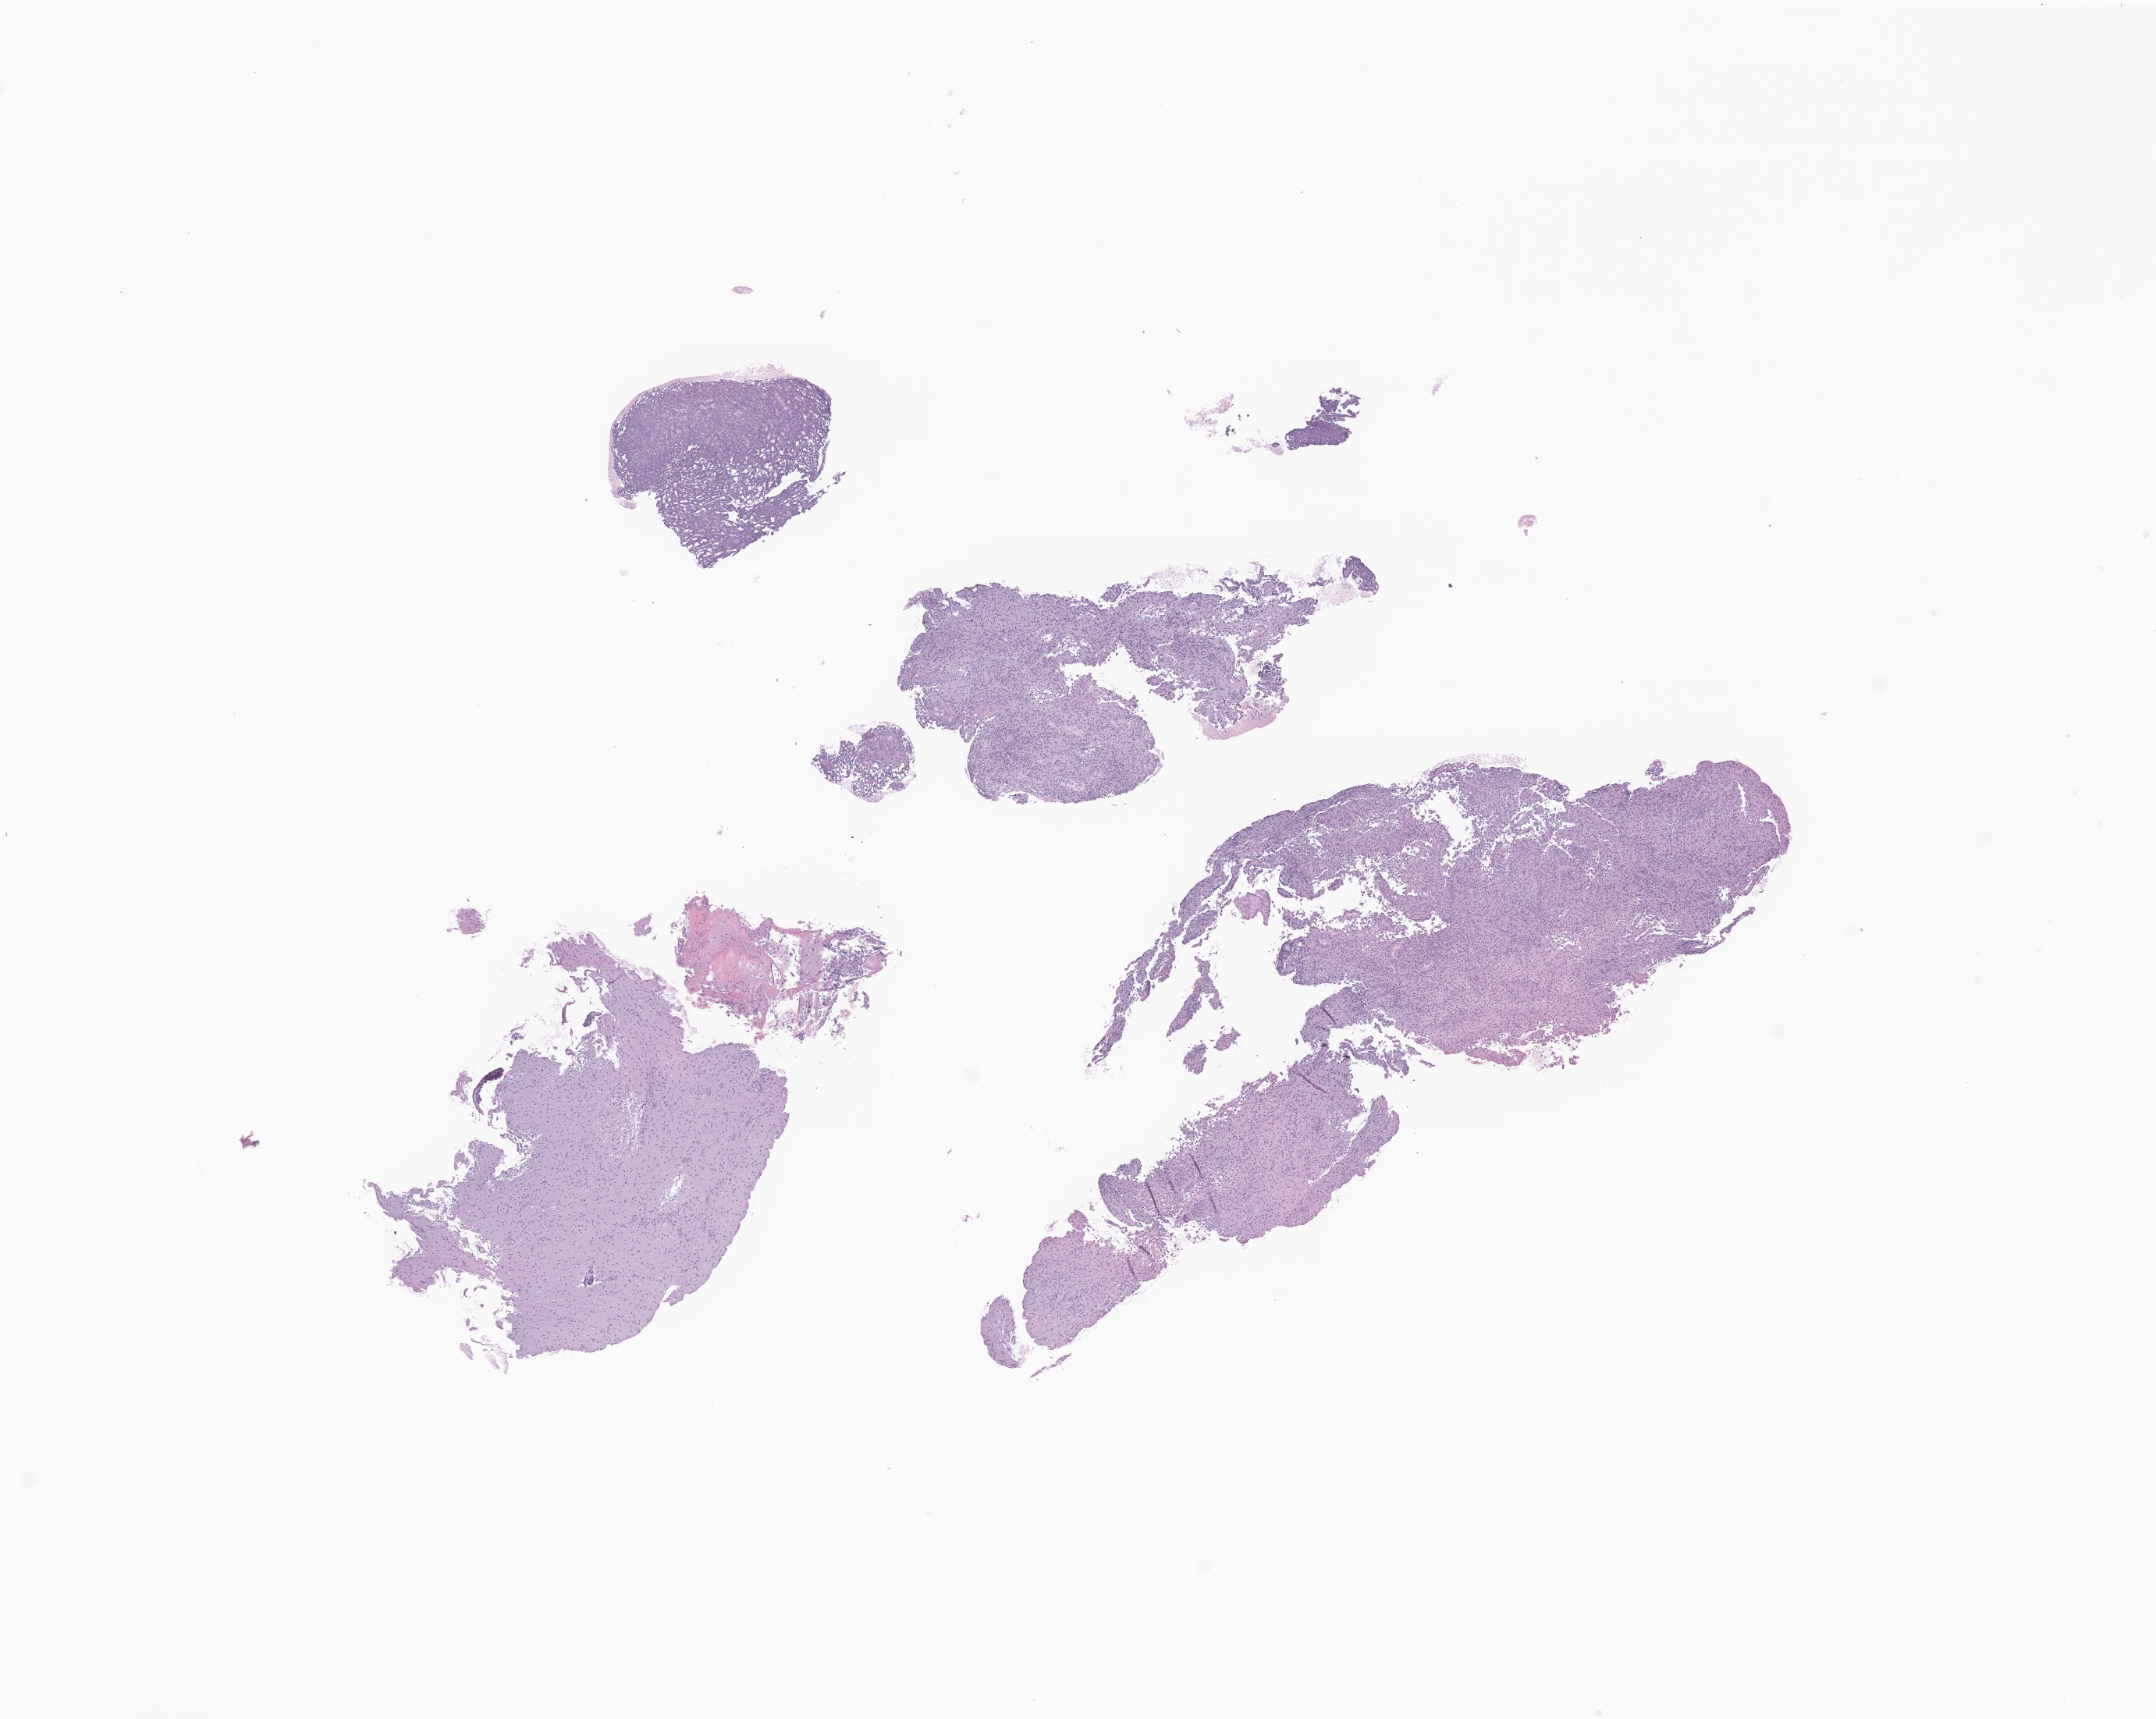
Hematoxylin and eosin (H&E) whole-slide image of tumor tissue from the brain stem, shown as a low-resolution overview of the whole scanned area (about 11.6 x 9.3 mm); formalin-fixed, paraffin-embedded (FFPE) tissue. Male patient, age 106 months (8 years 10 months).
Diagnosis: Glioma, malignant.